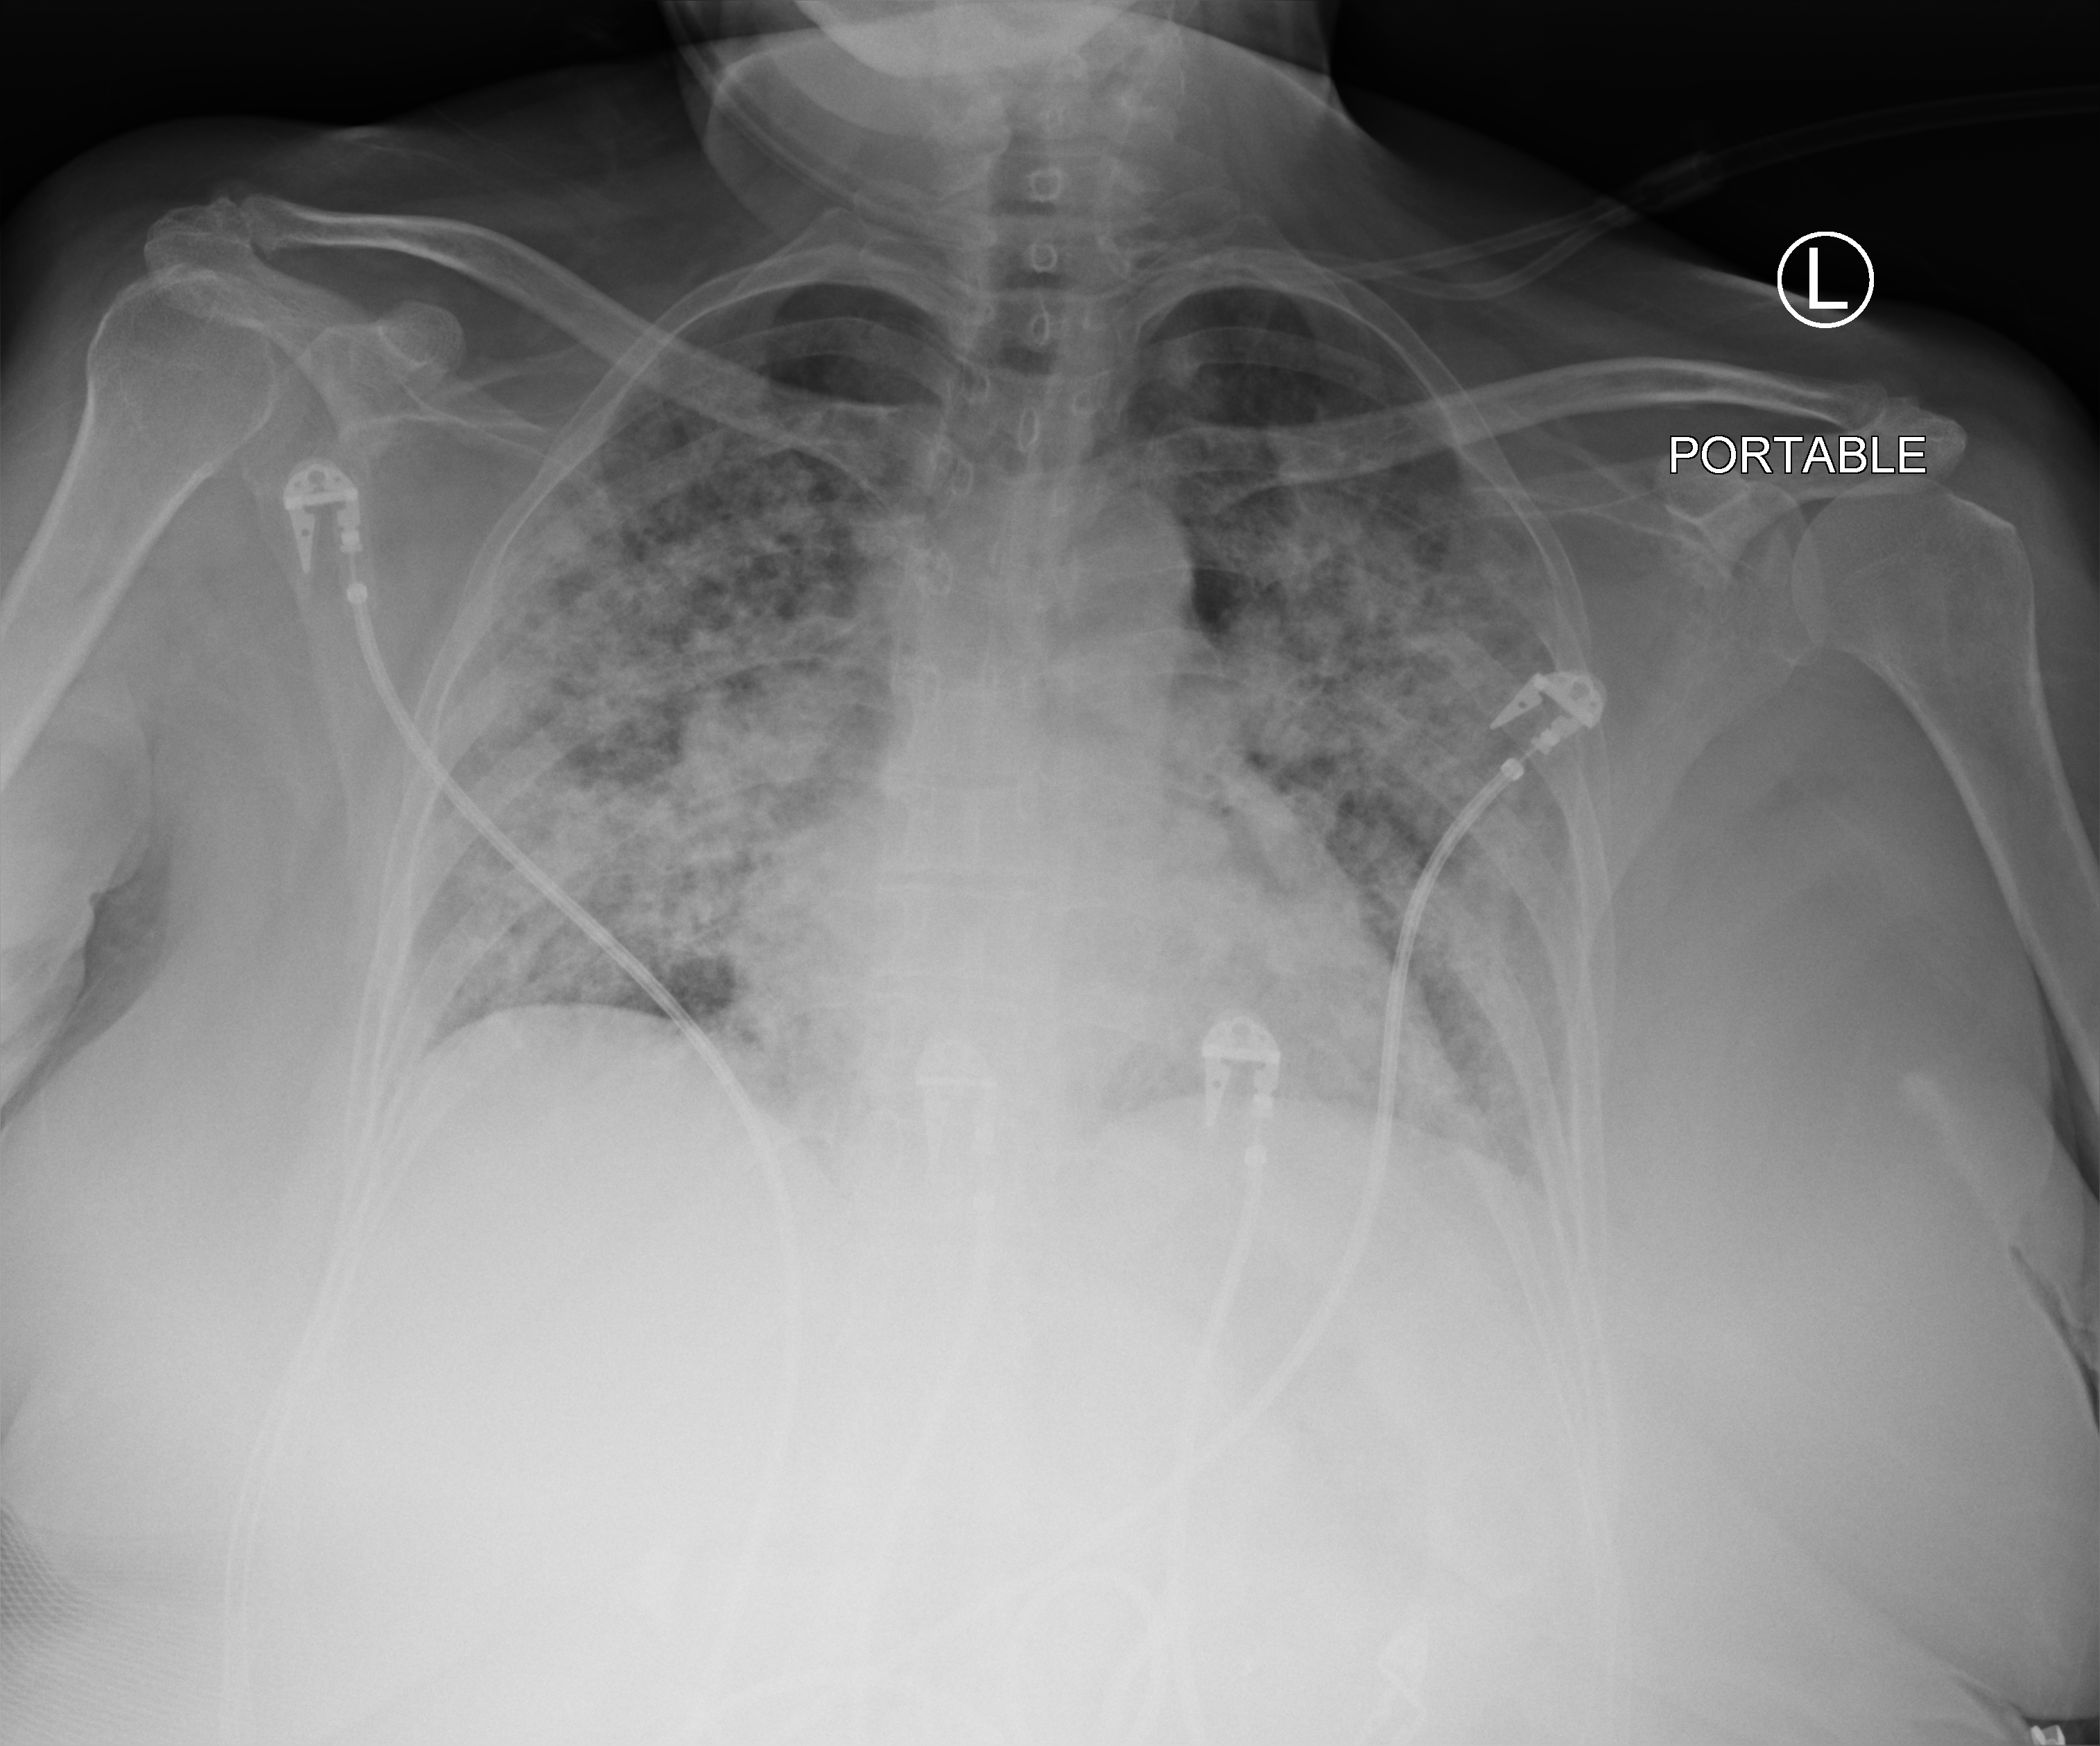
Portable chest radiograph, anteroposterior (AP) projection. Patient hospitalised with COVID-19; female, aged 18–59 years.
From the hospital-stay record, not from the radiograph (when in the stay this image was taken is not recorded): admitted to intensive care during this hospital stay: no.